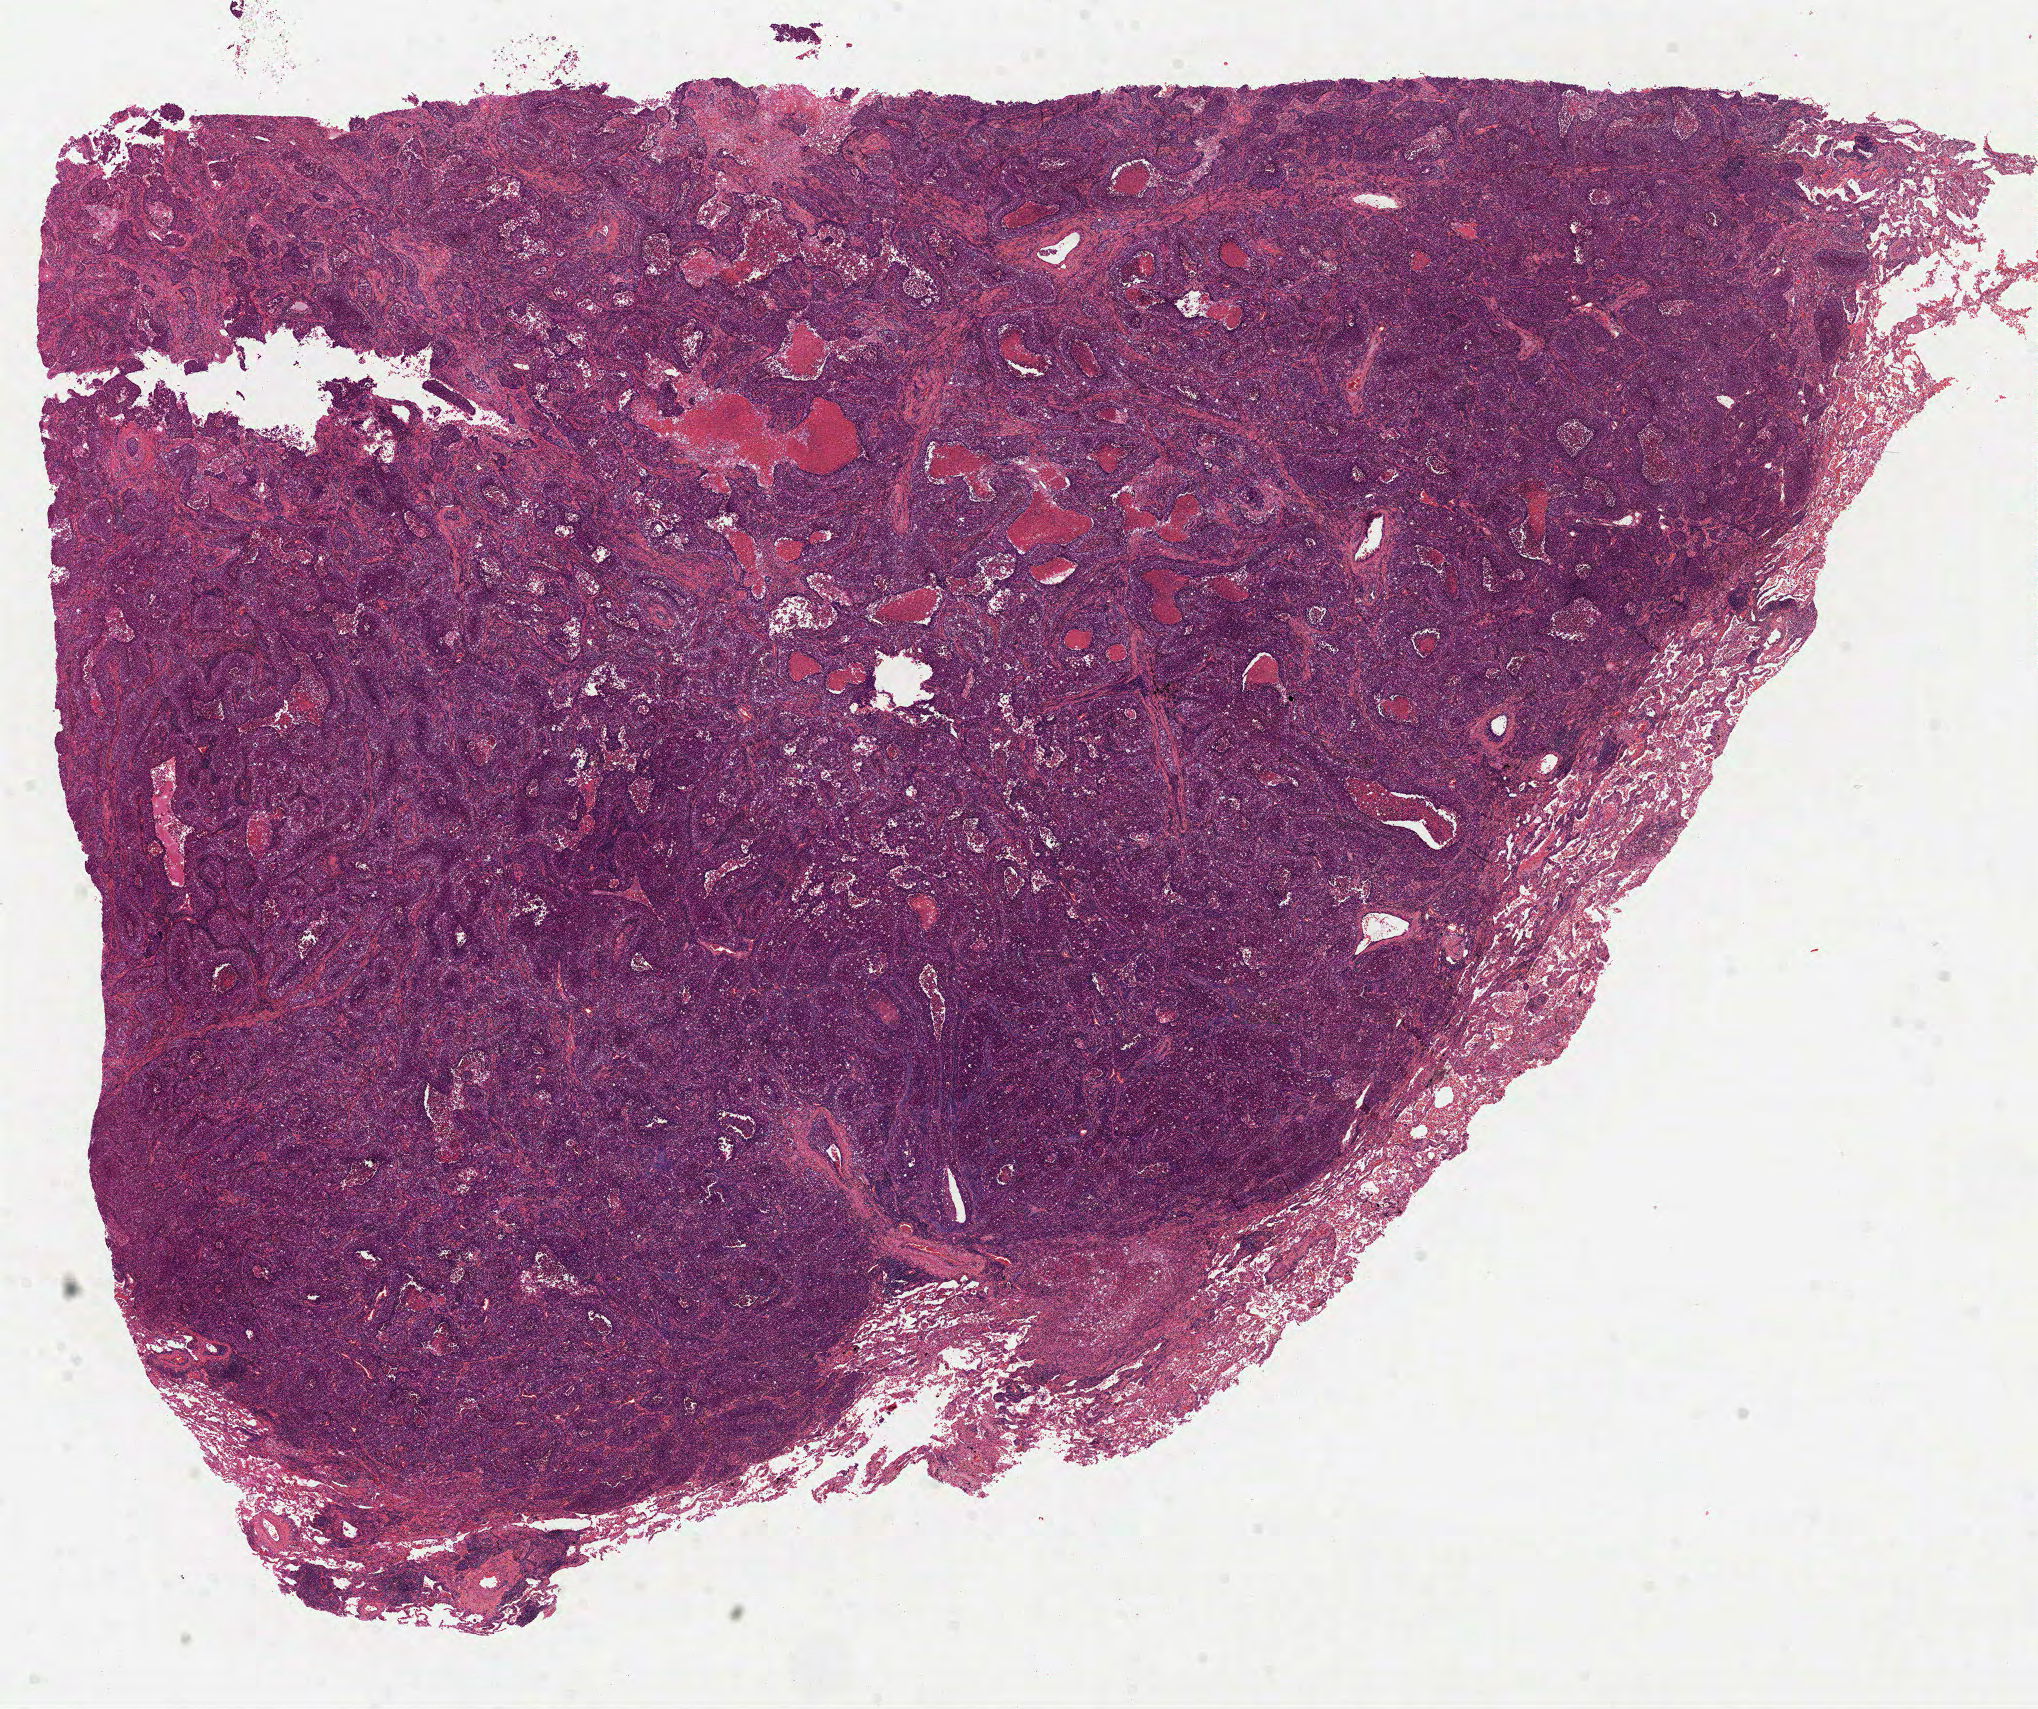
Digitized H&E-stained tissue section (whole slide) — a low-resolution overview of the entire scanned area, about 16.4 x 13.8 mm (slide scanned at 40x). FFPE section. Lung, primary tumour sample. Male, age 64 years at initial diagnosis.
* AJCC pathologic stage: IIIA
* diagnosis: Squamous cell carcinoma, NOS (upper lobe, lung)